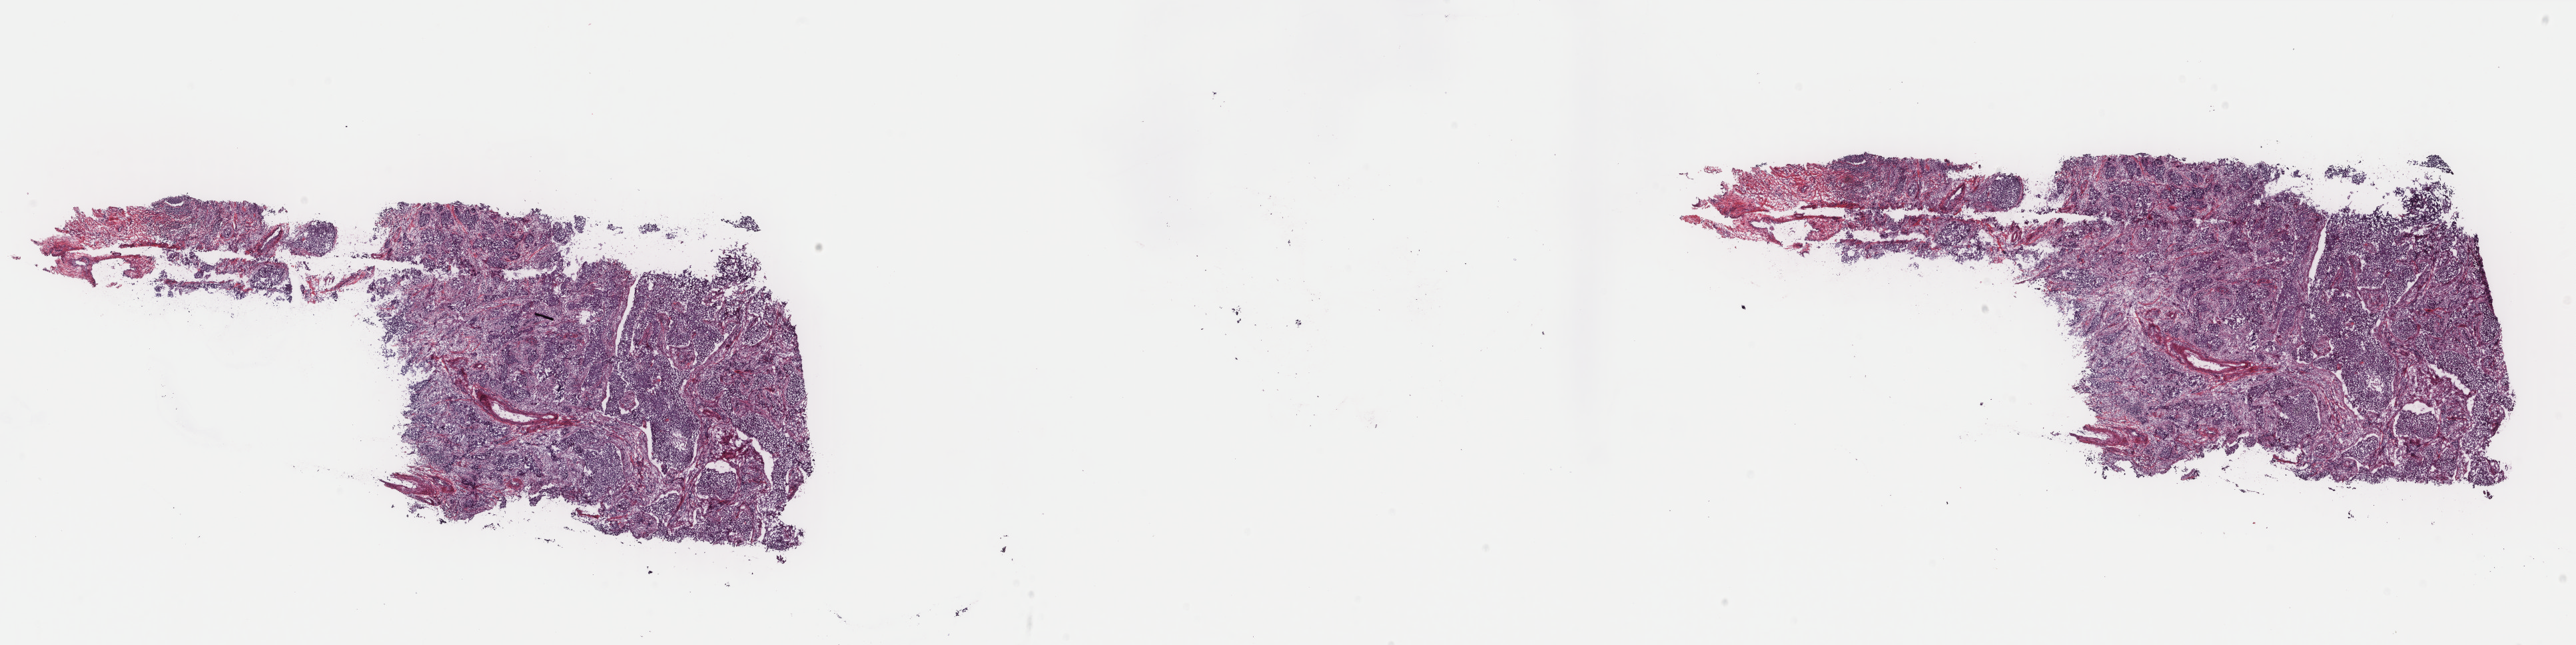
H&E-stained whole-slide image — a low-resolution overview of the entire scanned area, about 30.7 x 7.7 mm (from a 40x scan). Frozen section from the top of the tissue portion. Primary tumour sample from the cervix. Patient: female, age at initial diagnosis 50 years. Histologic grade: G2 (moderately differentiated). Slide review estimates, as recorded: tumour cells 100%, tumour nuclei 65%, normal cells 0%, stromal cells 0%, necrosis 0%. Infiltration values recorded for this section: lymphocyte infiltration 2%, monocyte infiltration 0%, neutrophil infiltration 0%.
• histologic diagnosis: Squamous cell carcinoma, NOS (cervix uteri)
• lymph nodes positive (case pathology): 0 of 13 examined
• FIGO stage: IB1